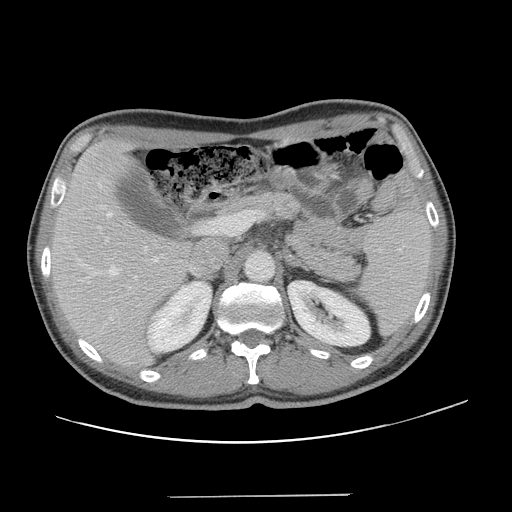
Contrast-enhanced abdominal CT, one axial slice. Position 81 of 131 along the scan axis. Intravenous contrast given. Soft-tissue window (W 400 / L 40 HU). 2.5 mm slice thickness. 512 × 512 image matrix, field of view 403 × 403 mm. Male patient, age 60 years. Case-level facts recorded for this patient, not image findings: diagnosis: colorectal cancer liver metastases, imaged before liver resection; multiple liver metastases: no; largest metastasis: 2.5 cm; chemotherapy before resection: no.
Outlined on this slice (outlined manually by an expert reader):
- hepatic veins: bounding box [x1, y1, x2, y2] px = [94, 183, 137, 288]
- liver: [52, 141, 188, 365]
- planned liver remnant (the part of the liver to remain after resection): [52, 141, 188, 358]
- portal vein (with intrahepatic branches): [151, 221, 214, 263]